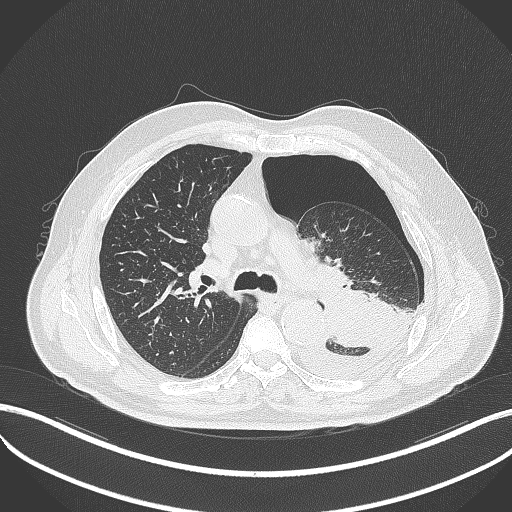
Chest CT, one axial slice. Reconstruction kernel B70f. Lung window (W 1500 / L -600 HU). 512 × 512 image matrix. Patient: male, 76 years. Case-level facts recorded for this patient, not image findings: clinical TNM (as recorded): T3 N0 M1b.
Outlined on this slice (bounding box drawn by a radiologist):
- lung tumour (recorded histology: adenocarcinoma): bounding box (x1, y1, x2, y2) in pixels: (315, 282, 401, 349)